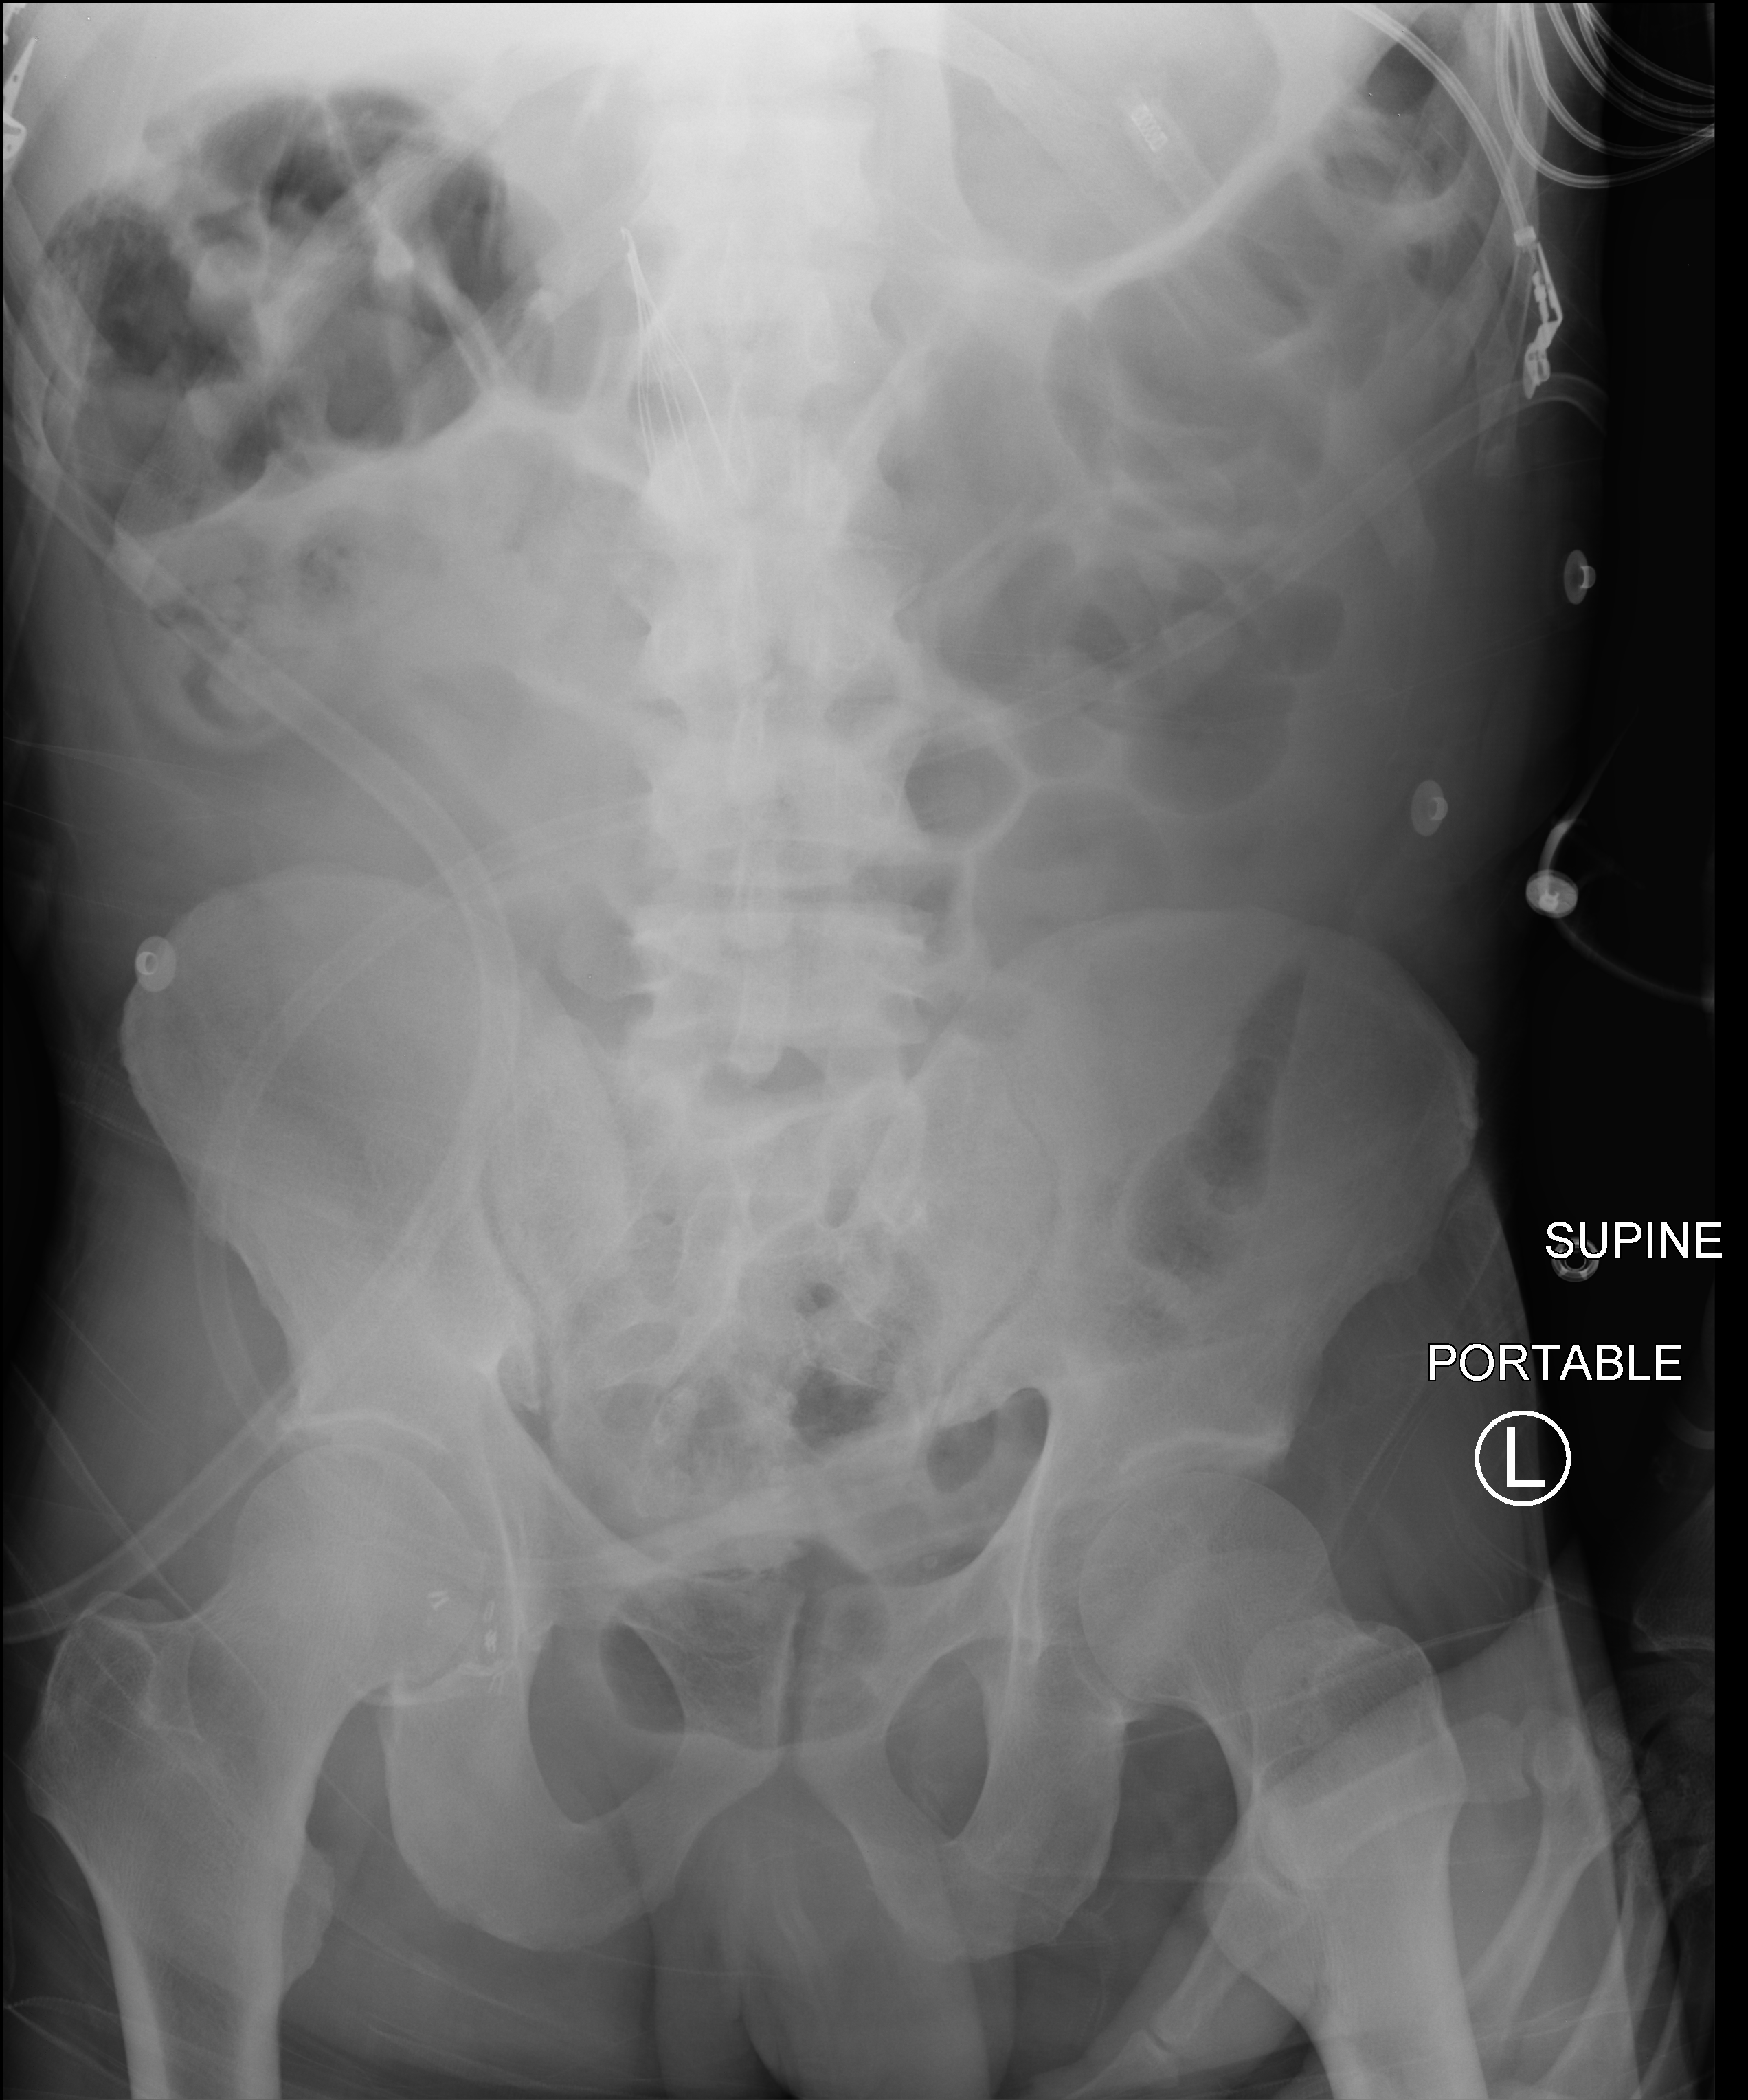
Abdomen X-ray (portable); anteroposterior (AP) projection. Male patient hospitalised with COVID-19, age 60–74 years.
Admission-level facts for this patient (not findings on this image; timing relative to this image not recorded): admitted to intensive care during this hospital stay: yes; other chronic lung disease (admission record): no; mechanically ventilated during this hospital stay: yes.